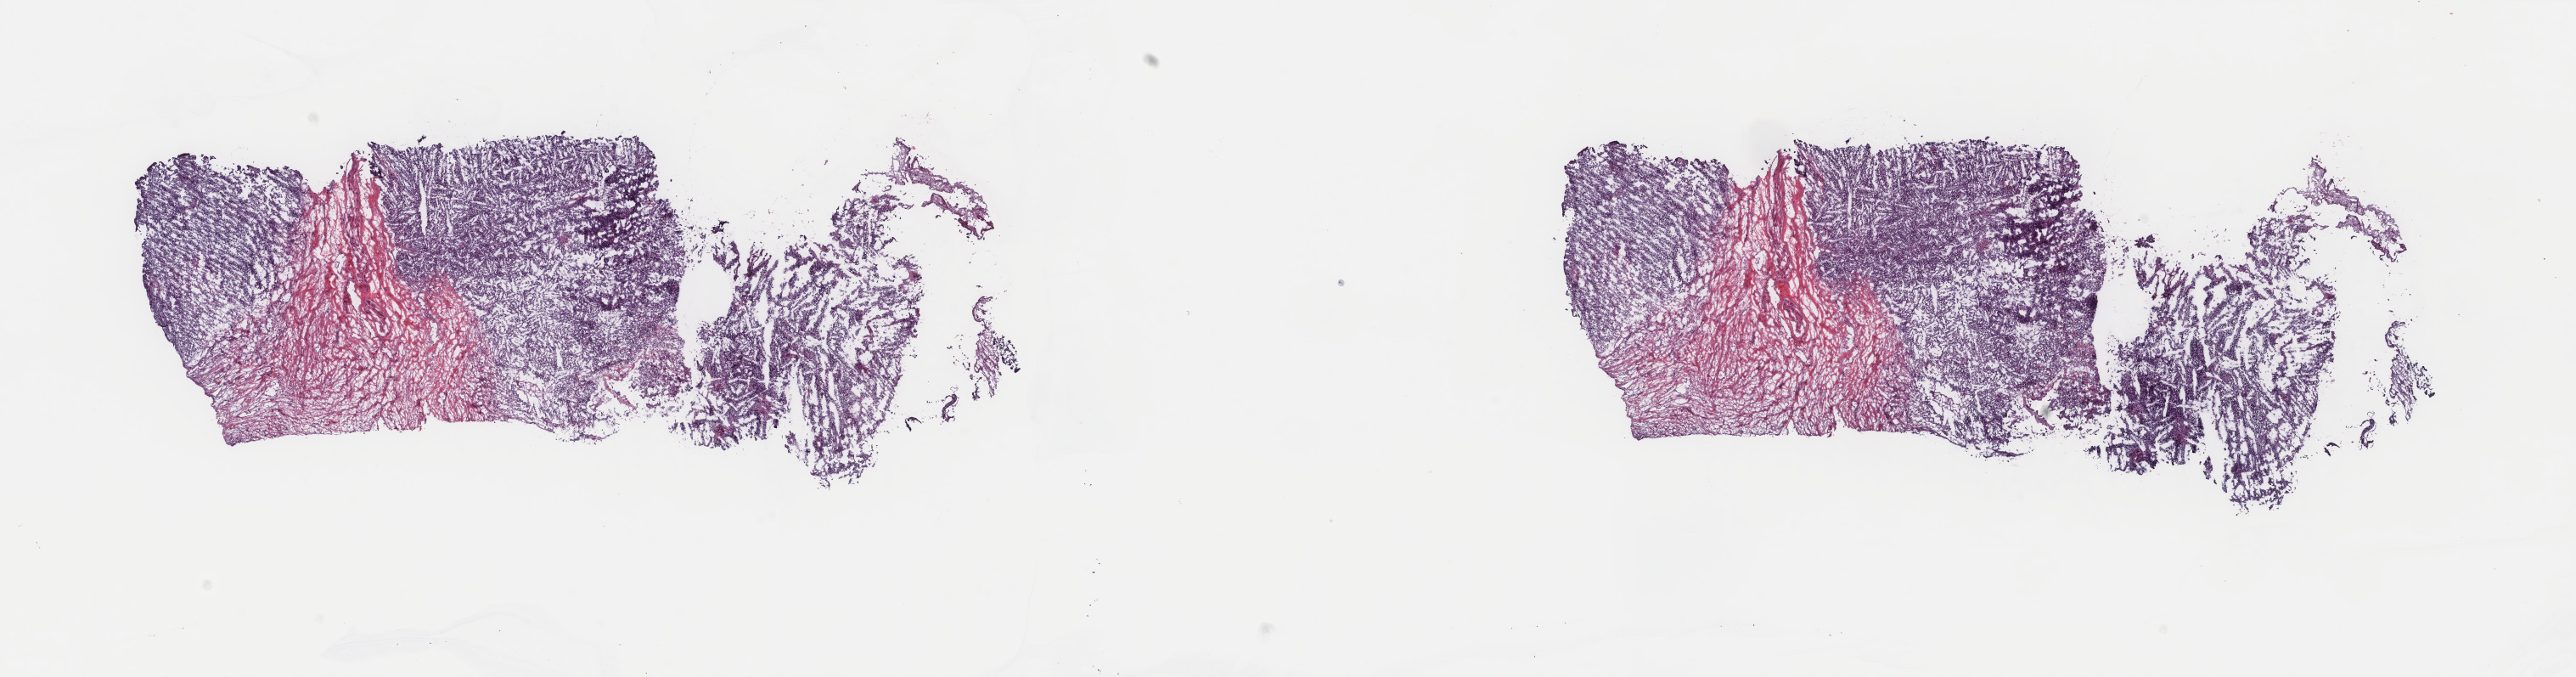
Digitized Hematoxylin and eosin (H&E) stained tissue section (whole slide), low-resolution overview of the scanned area, about 24.1 x 6.3 mm, frozen section, metastatic tumour sample, sampled site not recorded. Patient: male, age at initial diagnosis 60 years. Pathologist review of this section (percent, as recorded): tumour cells 70%, tumour nuclei 90%, normal cells 0%, stromal cells 30%, necrosis 0%. Infiltration values recorded for this section: lymphocyte infiltration 0%, monocyte infiltration 0%, neutrophil infiltration 0%.
This section: metastatic tumour tissue. Patient diagnosis: Malignant melanoma, NOS.